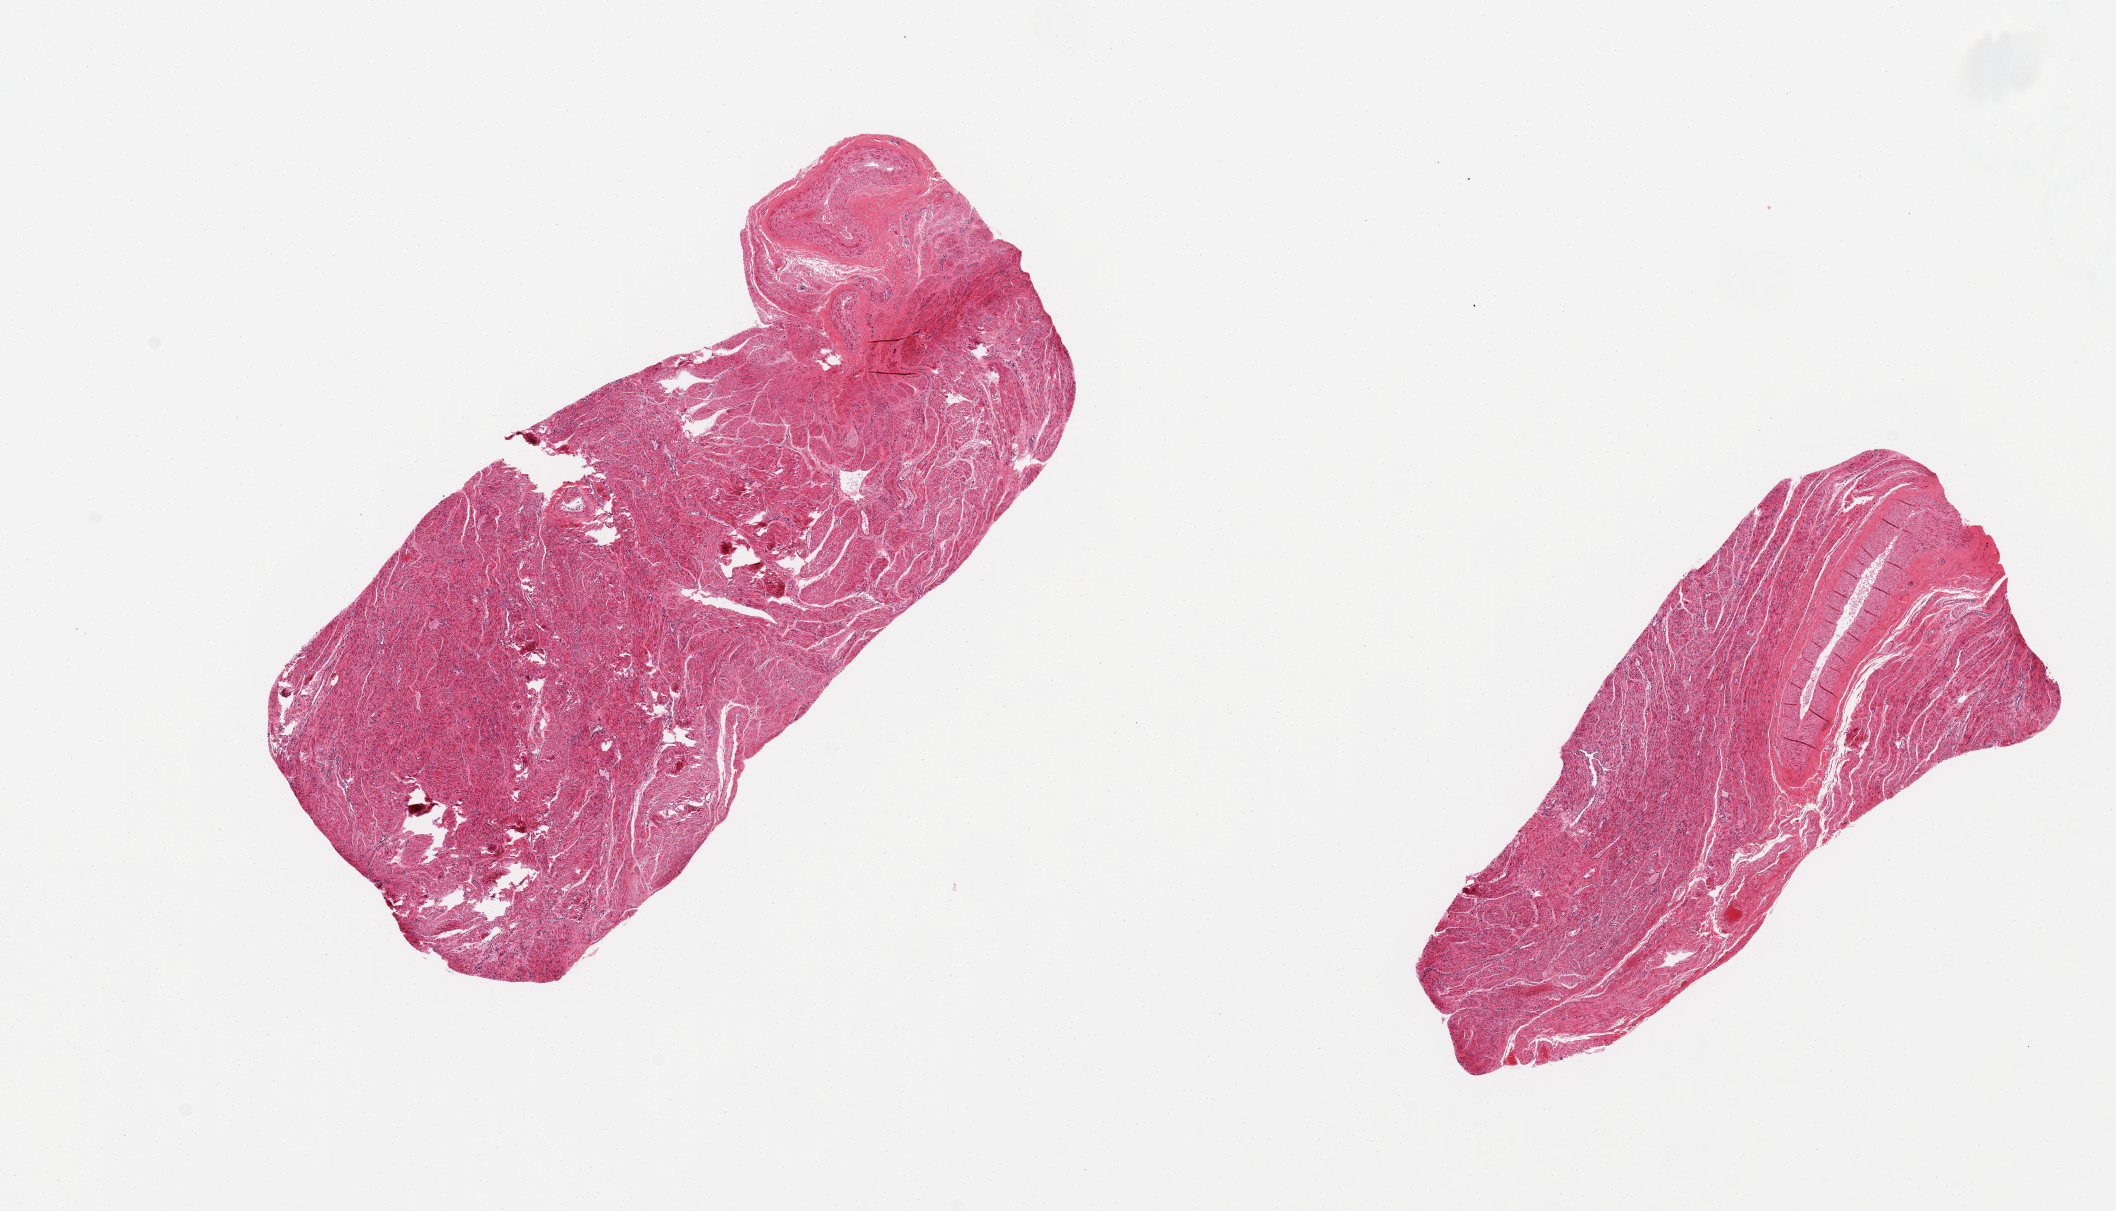
Haematoxylin and eosin whole-slide image, brightfield — a low-resolution overview of the entire scanned area, about 16.7 x 9.6 mm (slide scanned at 20x); PAXgene-fixed, paraffin-embedded tissue; section of uterus (target tissue); tissue donor sample. Female donor.
Review note (as recorded): 2 ~6x3.5mm aliquots, all myometrium; no visible glandular components.